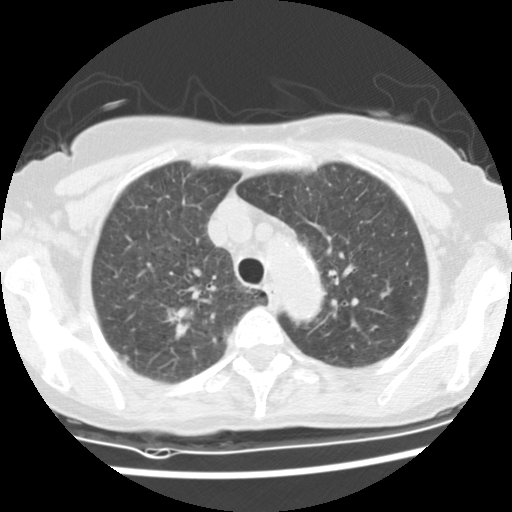
Low-dose screening chest CT, one axial slice. Position 107 of 134 along the scan axis. Lung window (W 1500 / L -600 HU). 512 × 512 image matrix, field of view 298 × 298 mm.
Structures marked on this image (expert manual segmentation):
- lesion 1 (tumor, upper lobe of right lung): box from (x=164, y=306) to (x=193, y=340) px